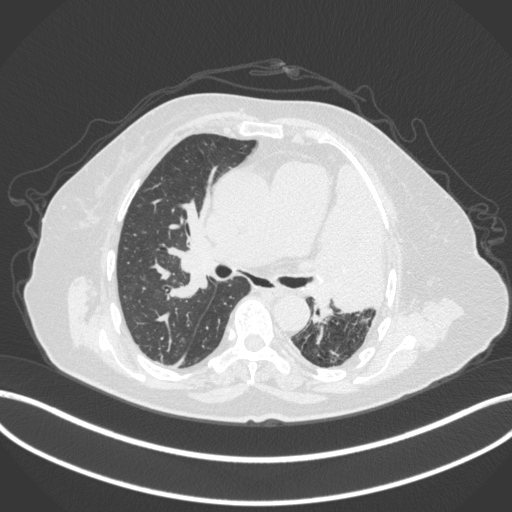
Chest CT, one axial slice; position 227 of 399 along the scan axis; reconstruction kernel B31f; 120 kVp; lung window (W 1500 / L -600 HU); 512 × 512 image matrix, field of view 400 × 400 mm. Female patient, age 75 years. Case-level facts recorded for this patient, not image findings: clinical TNM (as recorded): T3 N3 M1.
Annotated regions visible in this slice (rectangle marked by the reading radiologist):
- lung tumour (recorded histology: adenocarcinoma): bounding box (x1, y1, x2, y2) in pixels: (313, 157, 391, 313)